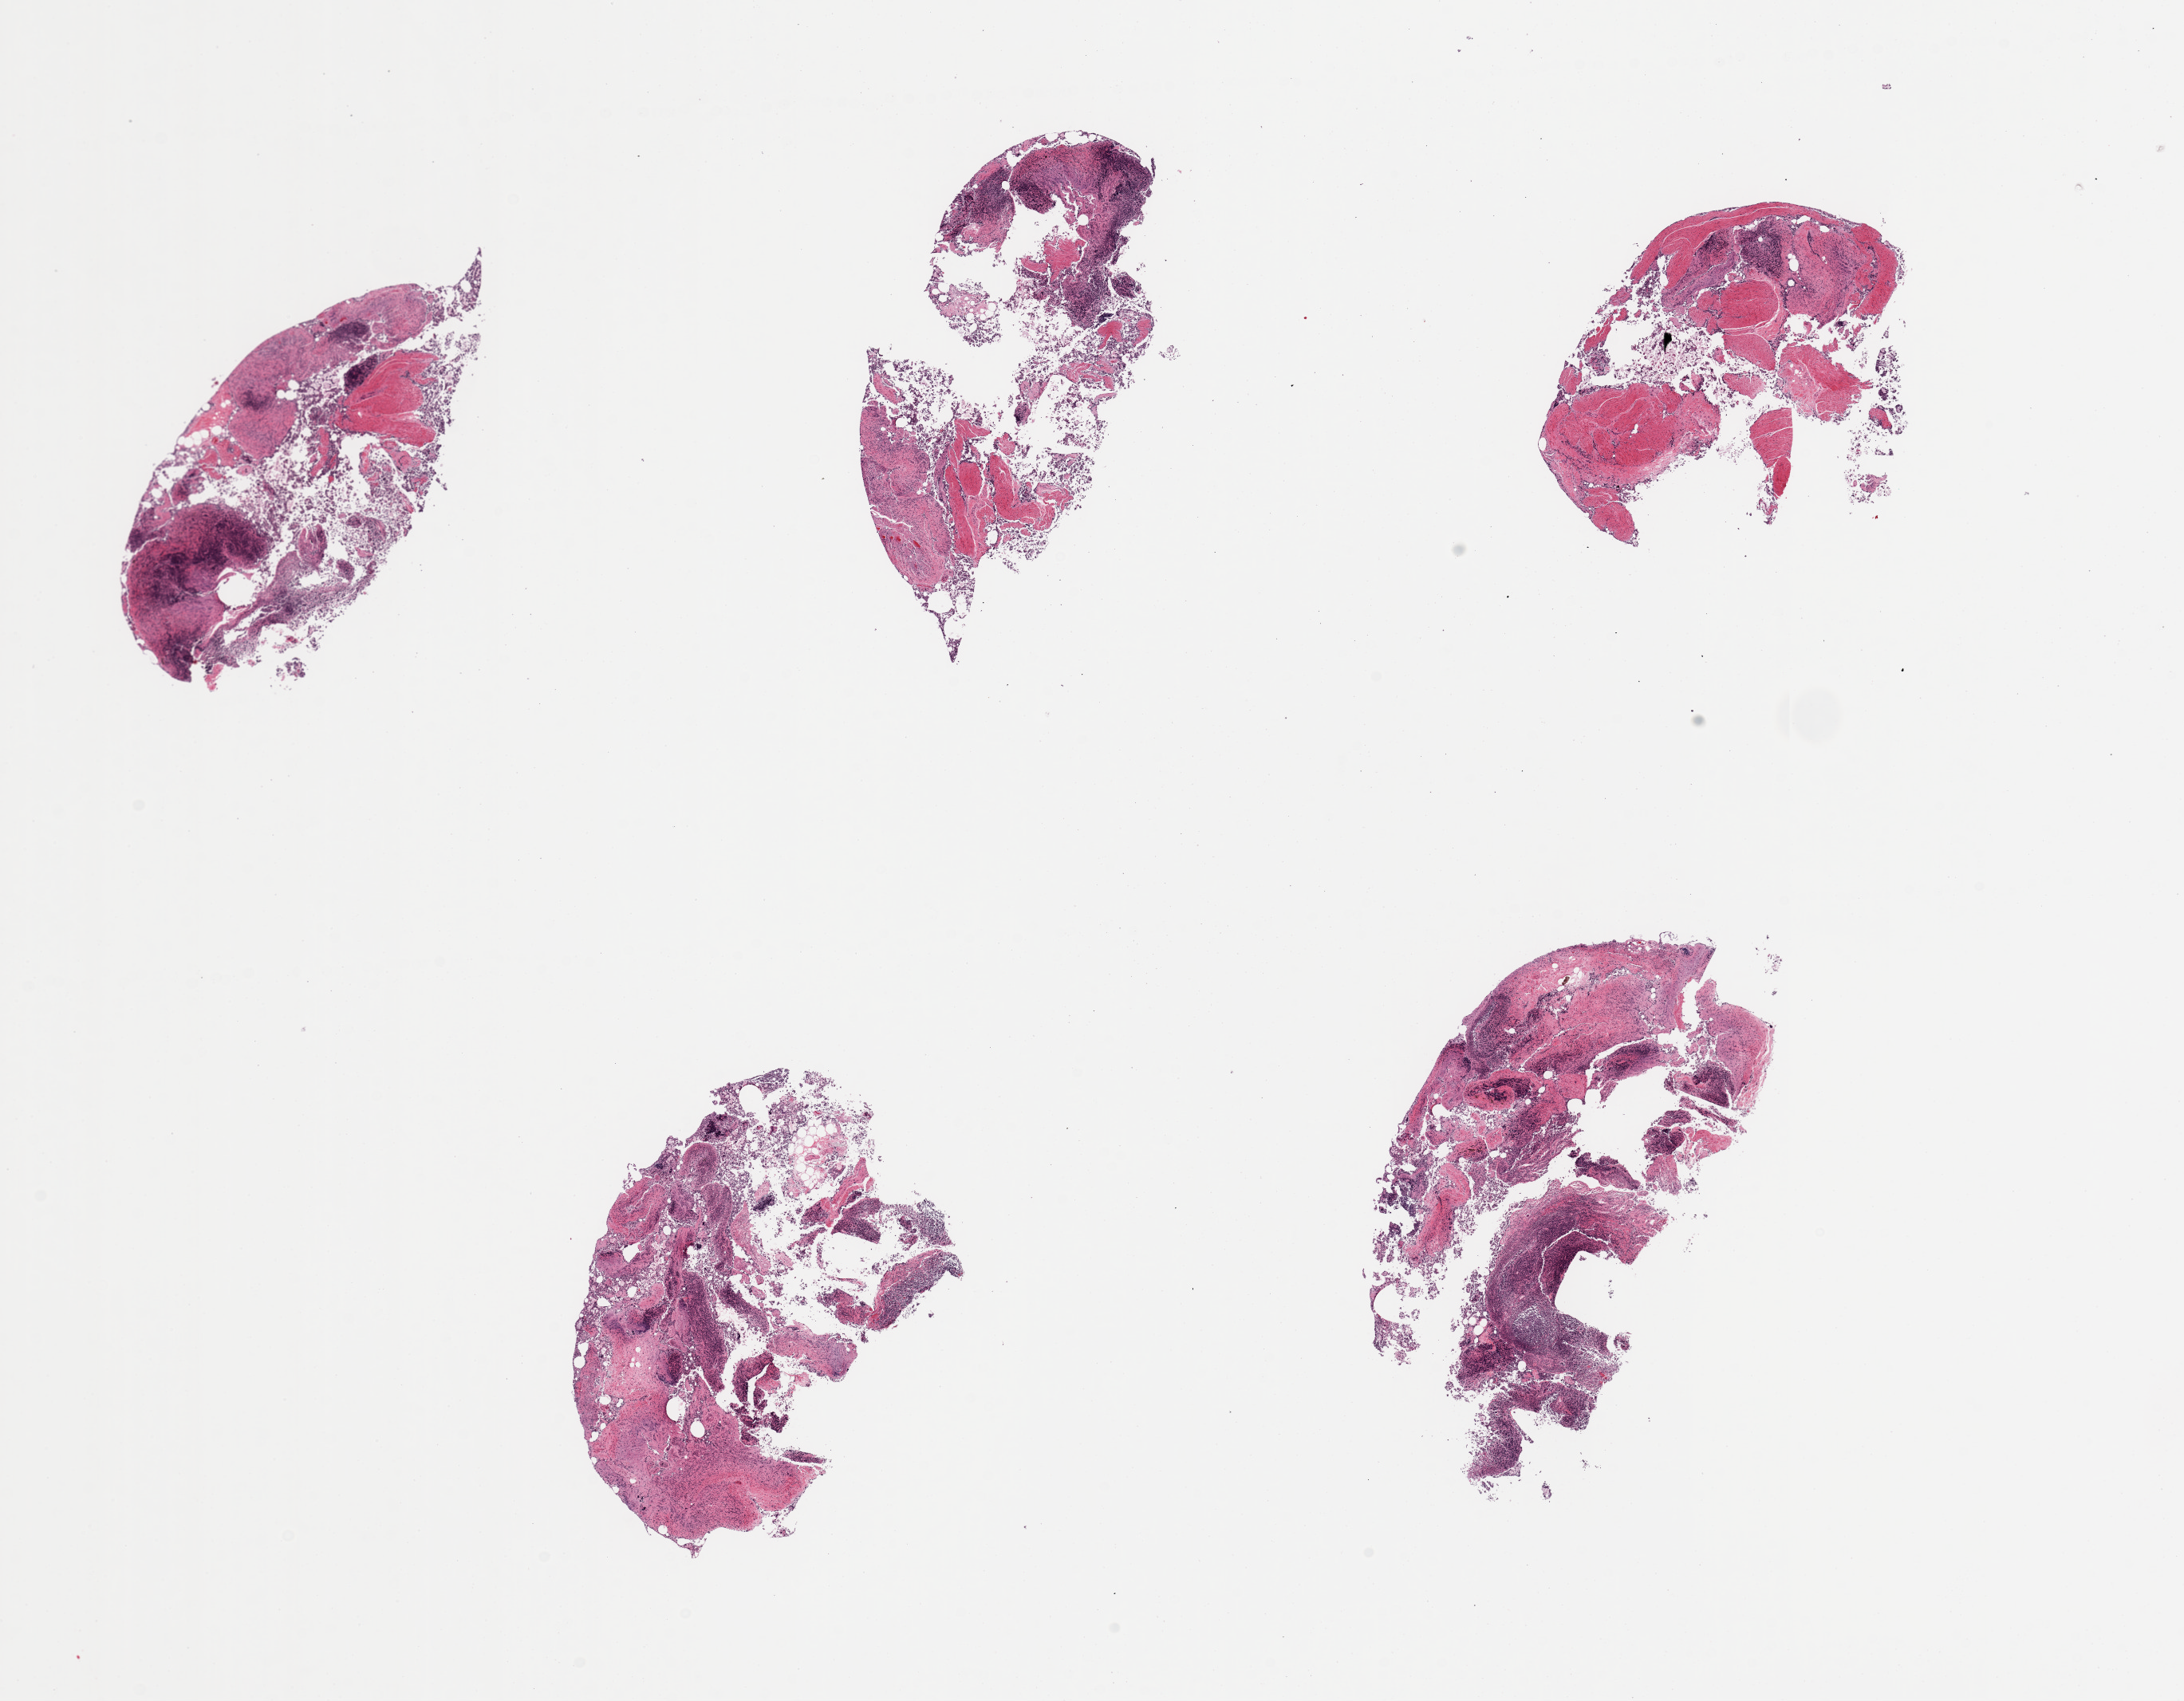
Whole-slide image, hematoxylin and eosin (H&E) stain, low-resolution overview of the scanned area, about 21.7 x 16.9 mm; PAXgene-fixed, paraffin-embedded tissue; target tissue: ileum; donor tissue sample. Donor sex: male.
Review note (as recorded): 5 pieces; Scattered collections of lymphoid tissue in autolyzed mucosa.